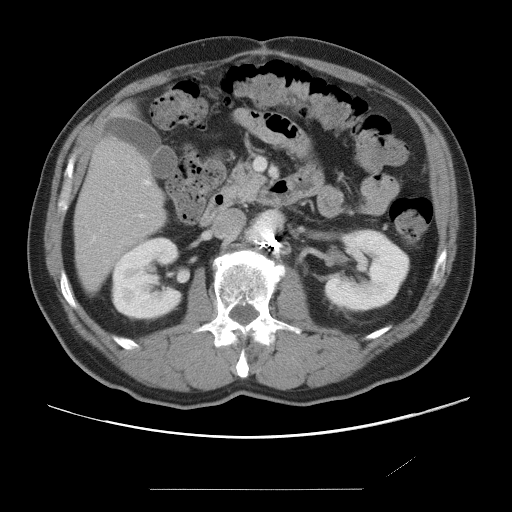
Contrast-enhanced abdominal CT, one axial slice; slice 26 of 87 in the series (ordered by position); 120 kVp; intravenous contrast given; soft-tissue window (W 400 / L 40 HU); 5 mm slice thickness; 512 × 512 image matrix, field of view 406 × 406 mm. Male patient, age 74 years. Case-level facts recorded for this patient, not image findings: diagnosis: colorectal cancer liver metastases, imaged before liver resection.
Outlined on this slice (outlined manually by an expert reader):
- hepatic veins: bounding box <93,180,150,240> (left, top, right, bottom; pixels)
- liver: <74,140,165,291>
- planned liver remnant (the part of the liver to remain after resection): <74,140,165,292>
- portal vein (with intrahepatic branches): <140,214,144,218>